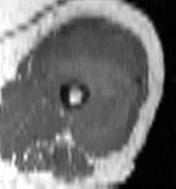
MRI of an extremity soft-tissue mass, one axial slice. Position 68 of 100 along the scan axis. MR volume resampled by the dataset authors to the PET/CT grid (not the native acquisition matrix). 176 × 189 image matrix. Female patient. From the clinical record (not read from this slice): histological type: undifferentiated – high grade; grade: high; site of the primary tumour: left thigh.
Structures marked on this image (expert contour drawn on MRI and transferred to this co-registered scan by the dataset authors):
- gross tumour volume including surrounding oedema: bounding box [x1, y1, x2, y2] px = [44, 27, 140, 158]
- gross tumour volume (mass): [44, 27, 138, 158]